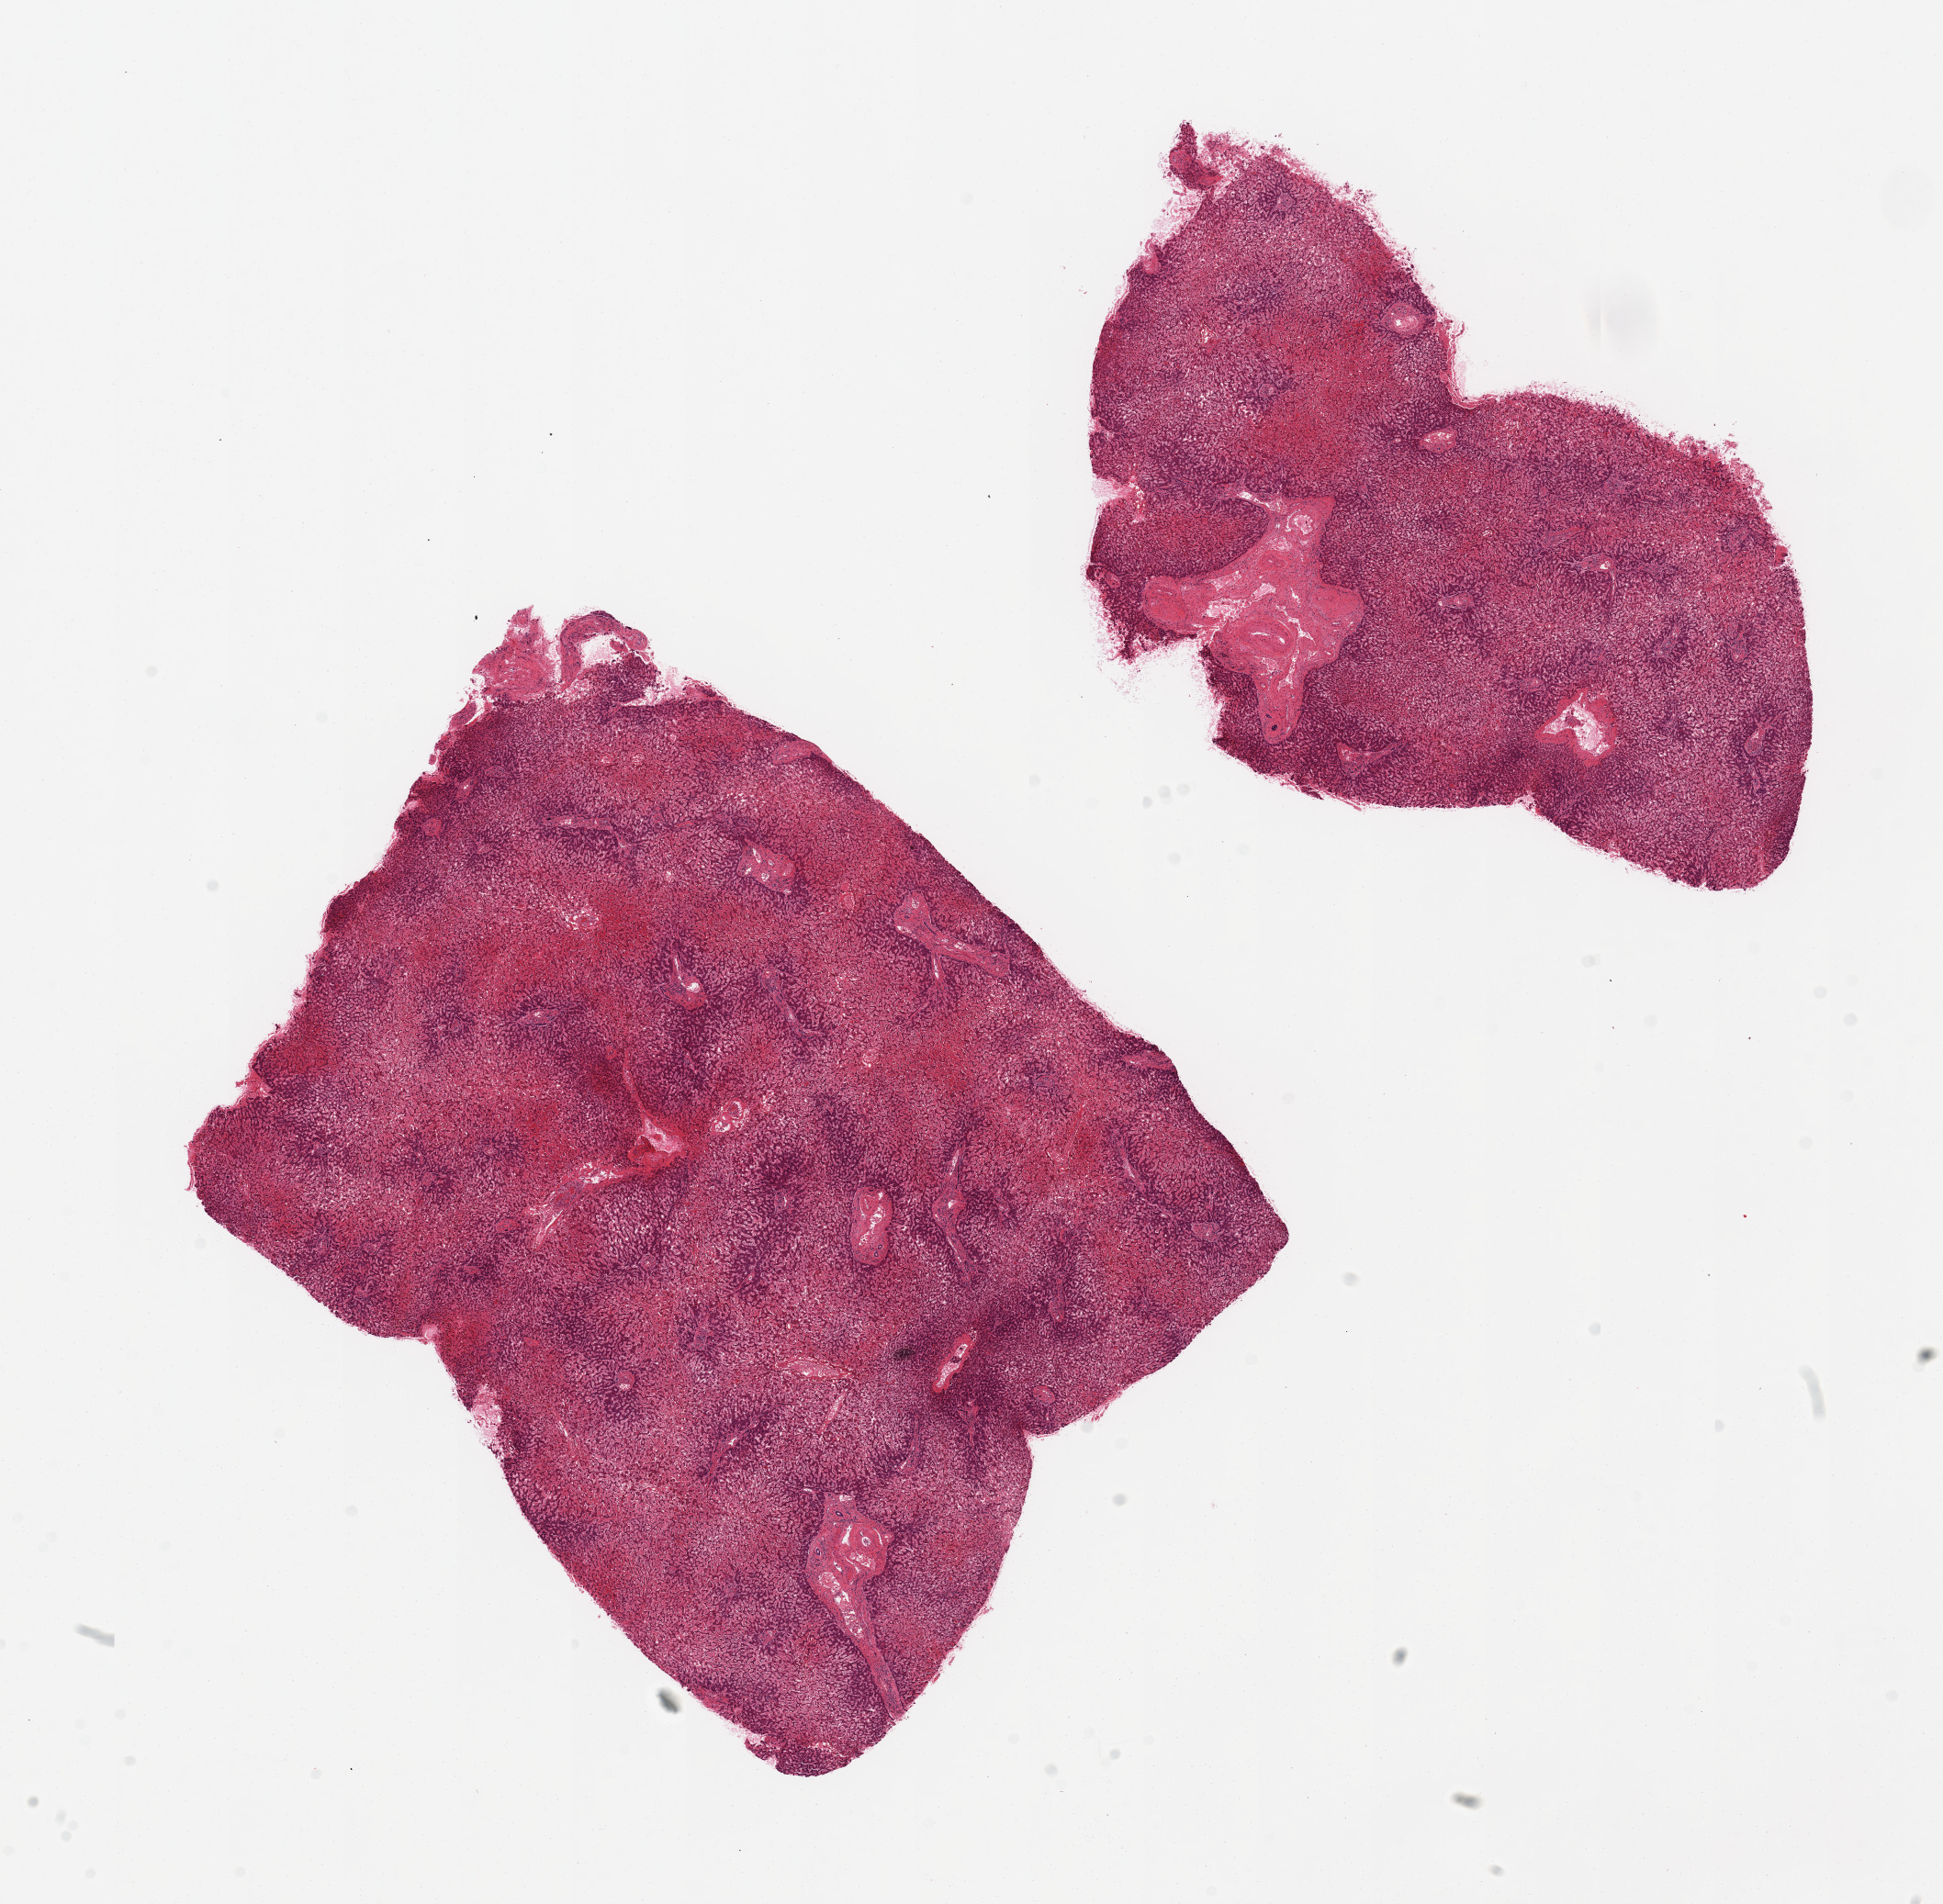
Haematoxylin and eosin whole-slide image — shown as a low-resolution overview of the whole scanned area (about 16.7 x 16.4 mm, from a 20x scan), PAXgene-fixed, paraffin-embedded tissue, section of liver (target tissue), tissue donor sample. Male donor.
• reviewer comment on this tissue sample: 2 pieces, marked centrilobular congestion/cardiac 'cirrhosis'